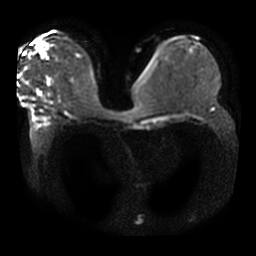
Breast MRI, one axial slice; position 18 of 42 along the scan axis; diffusion-weighted series; image 2 of 4 stored at this slice position (different b-values; order by instance number); 3 T; 5 mm slice thickness; 256 × 256 image matrix. Female patient.
Structures marked on this image (expert manual segmentation):
- tumour on diffusion-weighted imaging: bounding box (x1, y1, x2, y2) in pixels: (36, 43, 45, 52)